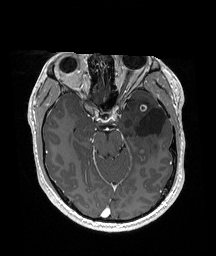
Brain MRI from a brain-tumour surgery series, one axial slice. Position 112 of 192 along the scan axis. T1-weighted post-contrast. 216 × 256 image matrix, field of view 211 × 250 mm. Case-level facts recorded for this patient, not image findings: histopathology: Glioneuronal tumor; WHO grade: 2; tumour location: Left Superior Temporal Gyrus.
Structures marked on this image (outlined manually by an expert reader):
- previous resection cavity: bounding box [x1, y1, x2, y2] px = [136, 108, 166, 136]
- tumour: [140, 104, 148, 154]